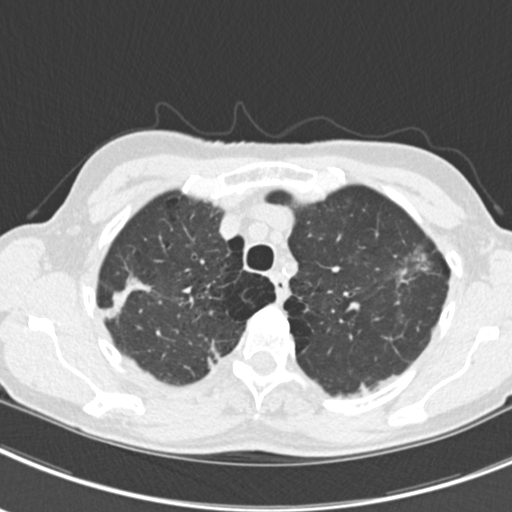
Axial slice from a low-dose chest CT screening exam. Second screening round (one year after baseline). Lung window (W 1500 / L -600 HU). 2 mm slice thickness. Slice 45 of 219 in the series. Female, age 63 years at enrolment. Current smoker at enrolment.
Expert-annotated lung lesion, box from (x=386, y=235) to (x=454, y=299) px. The screening reader recorded 9 non-calcified nodules or masses ≥4 mm on this exam (left upper lobe, right upper lobe, left upper lobe, left lower lobe, right middle lobe, left lower lobe, left lower lobe, right lower lobe, right lower lobe); which of them this box marks is not recorded. Official screen result: positive, other. Lung cancer was diagnosed 408 days after this screen: bronchiolo-alveolar adenocarcinoma, NOS, right upper lobe, right middle lobe, right lower lobe, left upper lobe, left lower lobe, moderately differentiated (G2), stage IV (AJCC 6th edition).